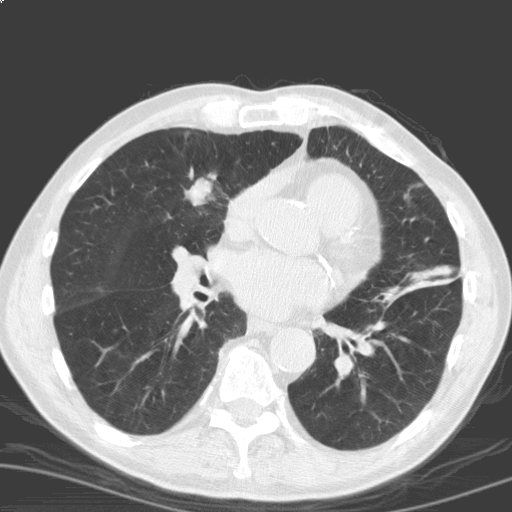
Axial slice from a low-dose chest CT screening exam; second screening round (one year after baseline); lung window (W 1500 / L -600 HU); 120 kVp; slice 95 of 184 in the series. Male participant, aged 69 years at enrolment. Current smoker at enrolment.
Expert-annotated lung lesion, box from (x=167, y=159) to (x=233, y=222) px. The screening reader recorded 2 non-calcified nodules or masses ≥4 mm on this exam; which of them this box marks is not recorded. Later outcome: lung cancer diagnosed 17 days after this screen — squamous cell carcinoma, NOS, right upper lobe, moderately differentiated (G2), stage IB (AJCC 6th edition), 40 mm at pathology.